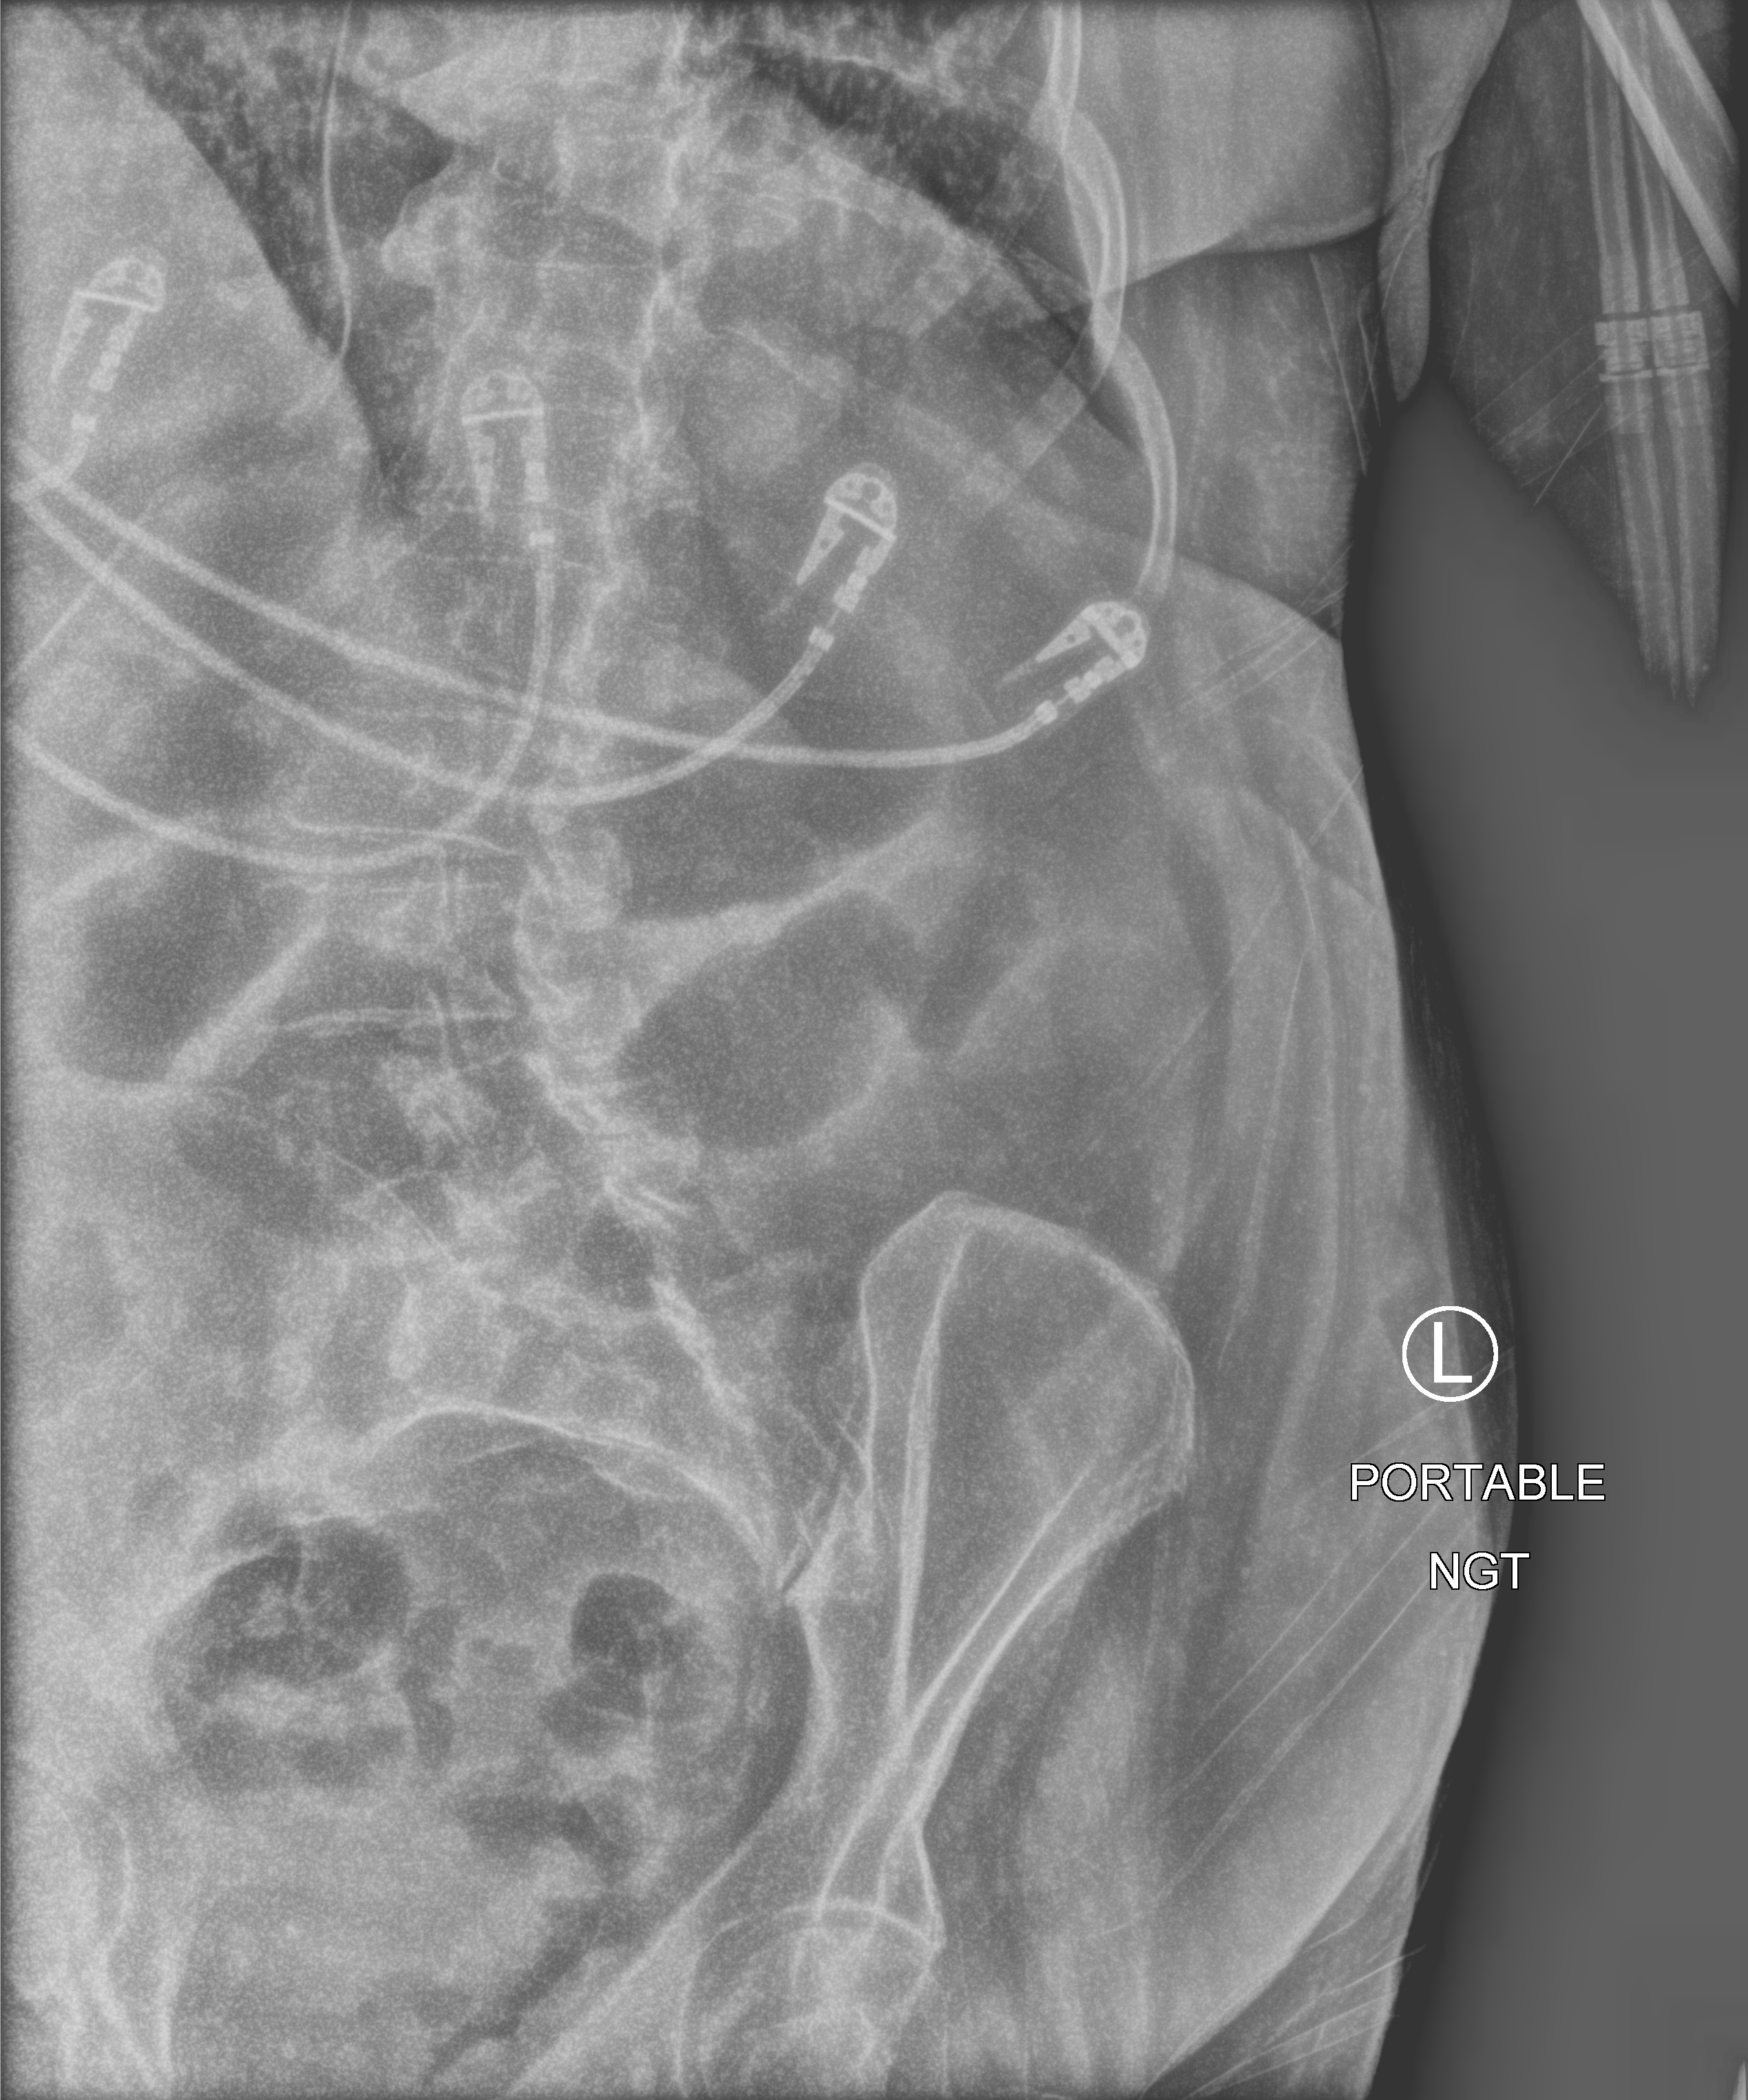
Bedside abdomen radiograph (computed radiography); anteroposterior (AP) projection. Patient hospitalised with COVID-19; female, aged 75–90 years.
From the hospital-stay record, not from the radiograph (when in the stay this image was taken is not recorded): length of hospital stay: 31 days; admitted to intensive care during this hospital stay: yes.